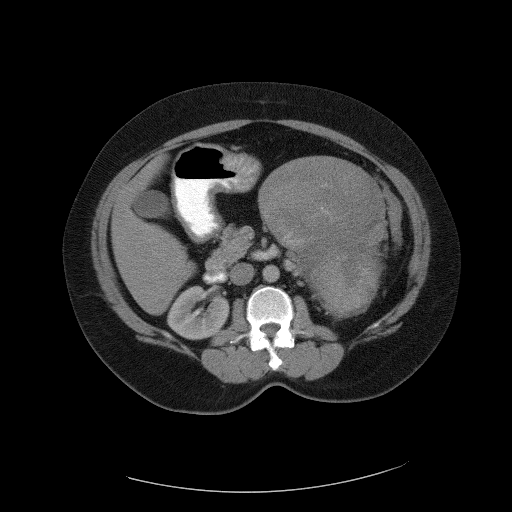
Contrast-enhanced abdominal CT, one axial slice. Slice 59 of 90 in the series (ordered by position). Intravenous contrast given. Soft-tissue window (W 400 / L 40 HU). 5 mm slice thickness. 512 × 512 image matrix. Patient: female, 55 years. From the clinical record (not read from this slice): diagnosis: adrenocortical carcinoma; tumour side: left adrenal; tumour size at pathology: 22 cm.
Outlined on this slice (semi-automatically segmented with operator editing):
- mass: box from (x=260, y=156) to (x=386, y=315) px